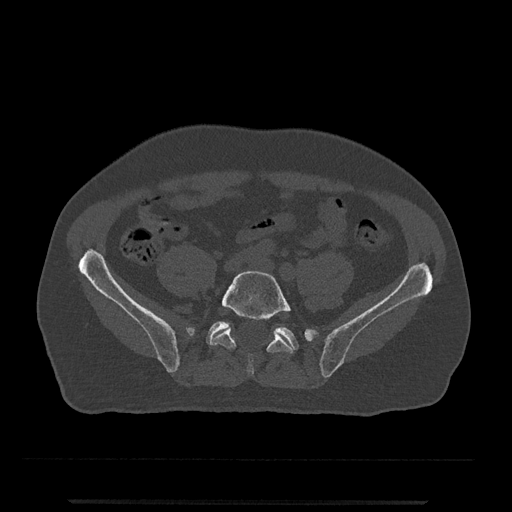
CT including the spine, one axial slice; slice 58 of 797 in the series (ordered by position); reconstruction kernel Br40s/3; bone window (W 1800 / L 400 HU); 0.5 mm slice thickness; 512 × 512 image matrix. Male patient, age 63 years. Case-level facts recorded for this patient, not image findings: primary cancer: prostate.
Annotated regions visible in this slice (semi-automatic segmentation, software-assisted and operator-edited):
- L5 vertebra: box from (x=210, y=270) to (x=293, y=375) px